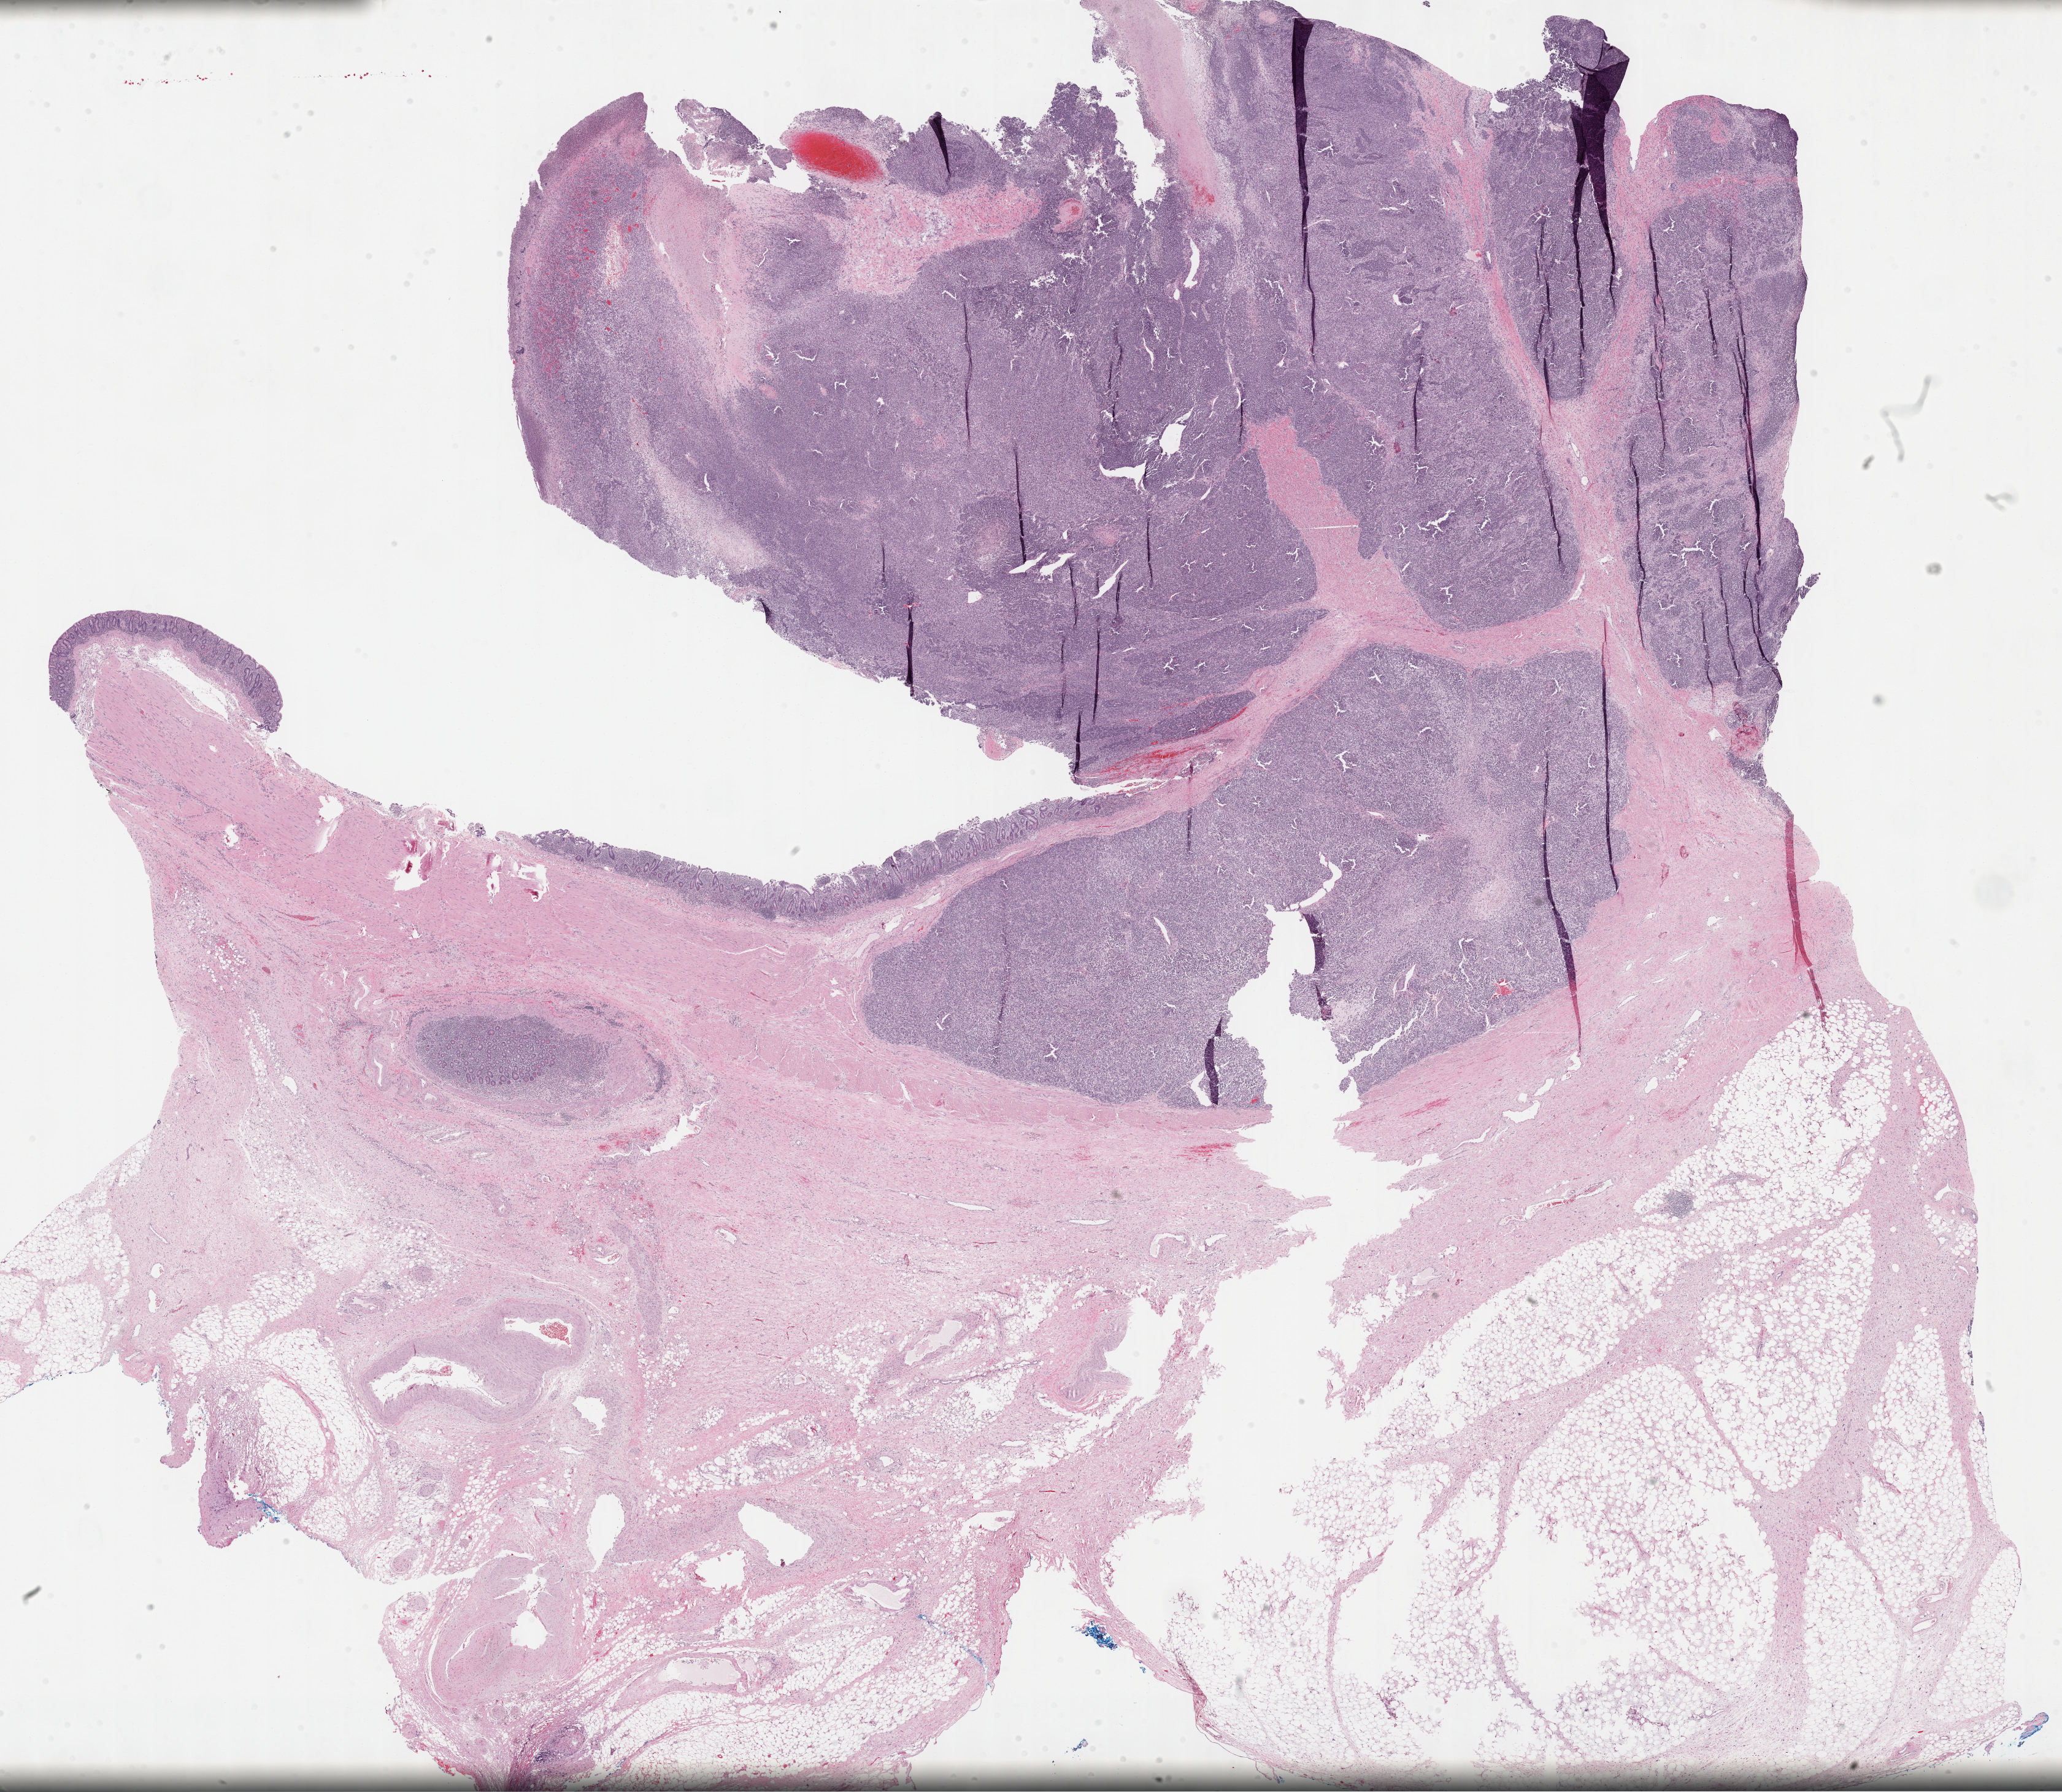
Digitized H&E tissue section (whole slide) — shown as a low-resolution overview of the whole scanned area (about 27.2 x 23.6 mm, slide scanned at 40x). Formalin-fixed paraffin-embedded (FFPE) diagnostic section. Primary tumour sample from the retroperitoneum and peritoneum. Patient: female, age at initial diagnosis 80 years.
Diagnosis: Dedifferentiated liposarcoma (retroperitoneum).